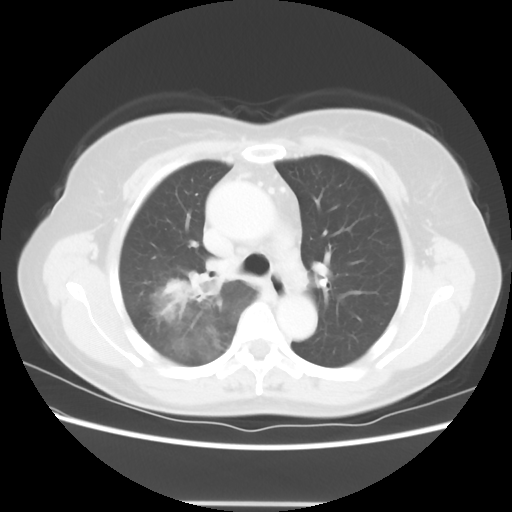
Chest CT, one axial slice; slice 40 of 56 in the series (ordered by position); lung window (W 1500 / L -600 HU); 5 mm slice thickness; 512 × 512 image matrix, field of view 360 × 360 mm. Female patient, age 55 years. From the clinical record (not read from this slice): clinical TNM (as recorded): T2 N1 M0; histopathological grade: G2-3.
Annotated regions visible in this slice (bounding box drawn by a radiologist):
- lung tumour (recorded histology: adenocarcinoma): bounding box [x1, y1, x2, y2] px = [142, 268, 233, 331]